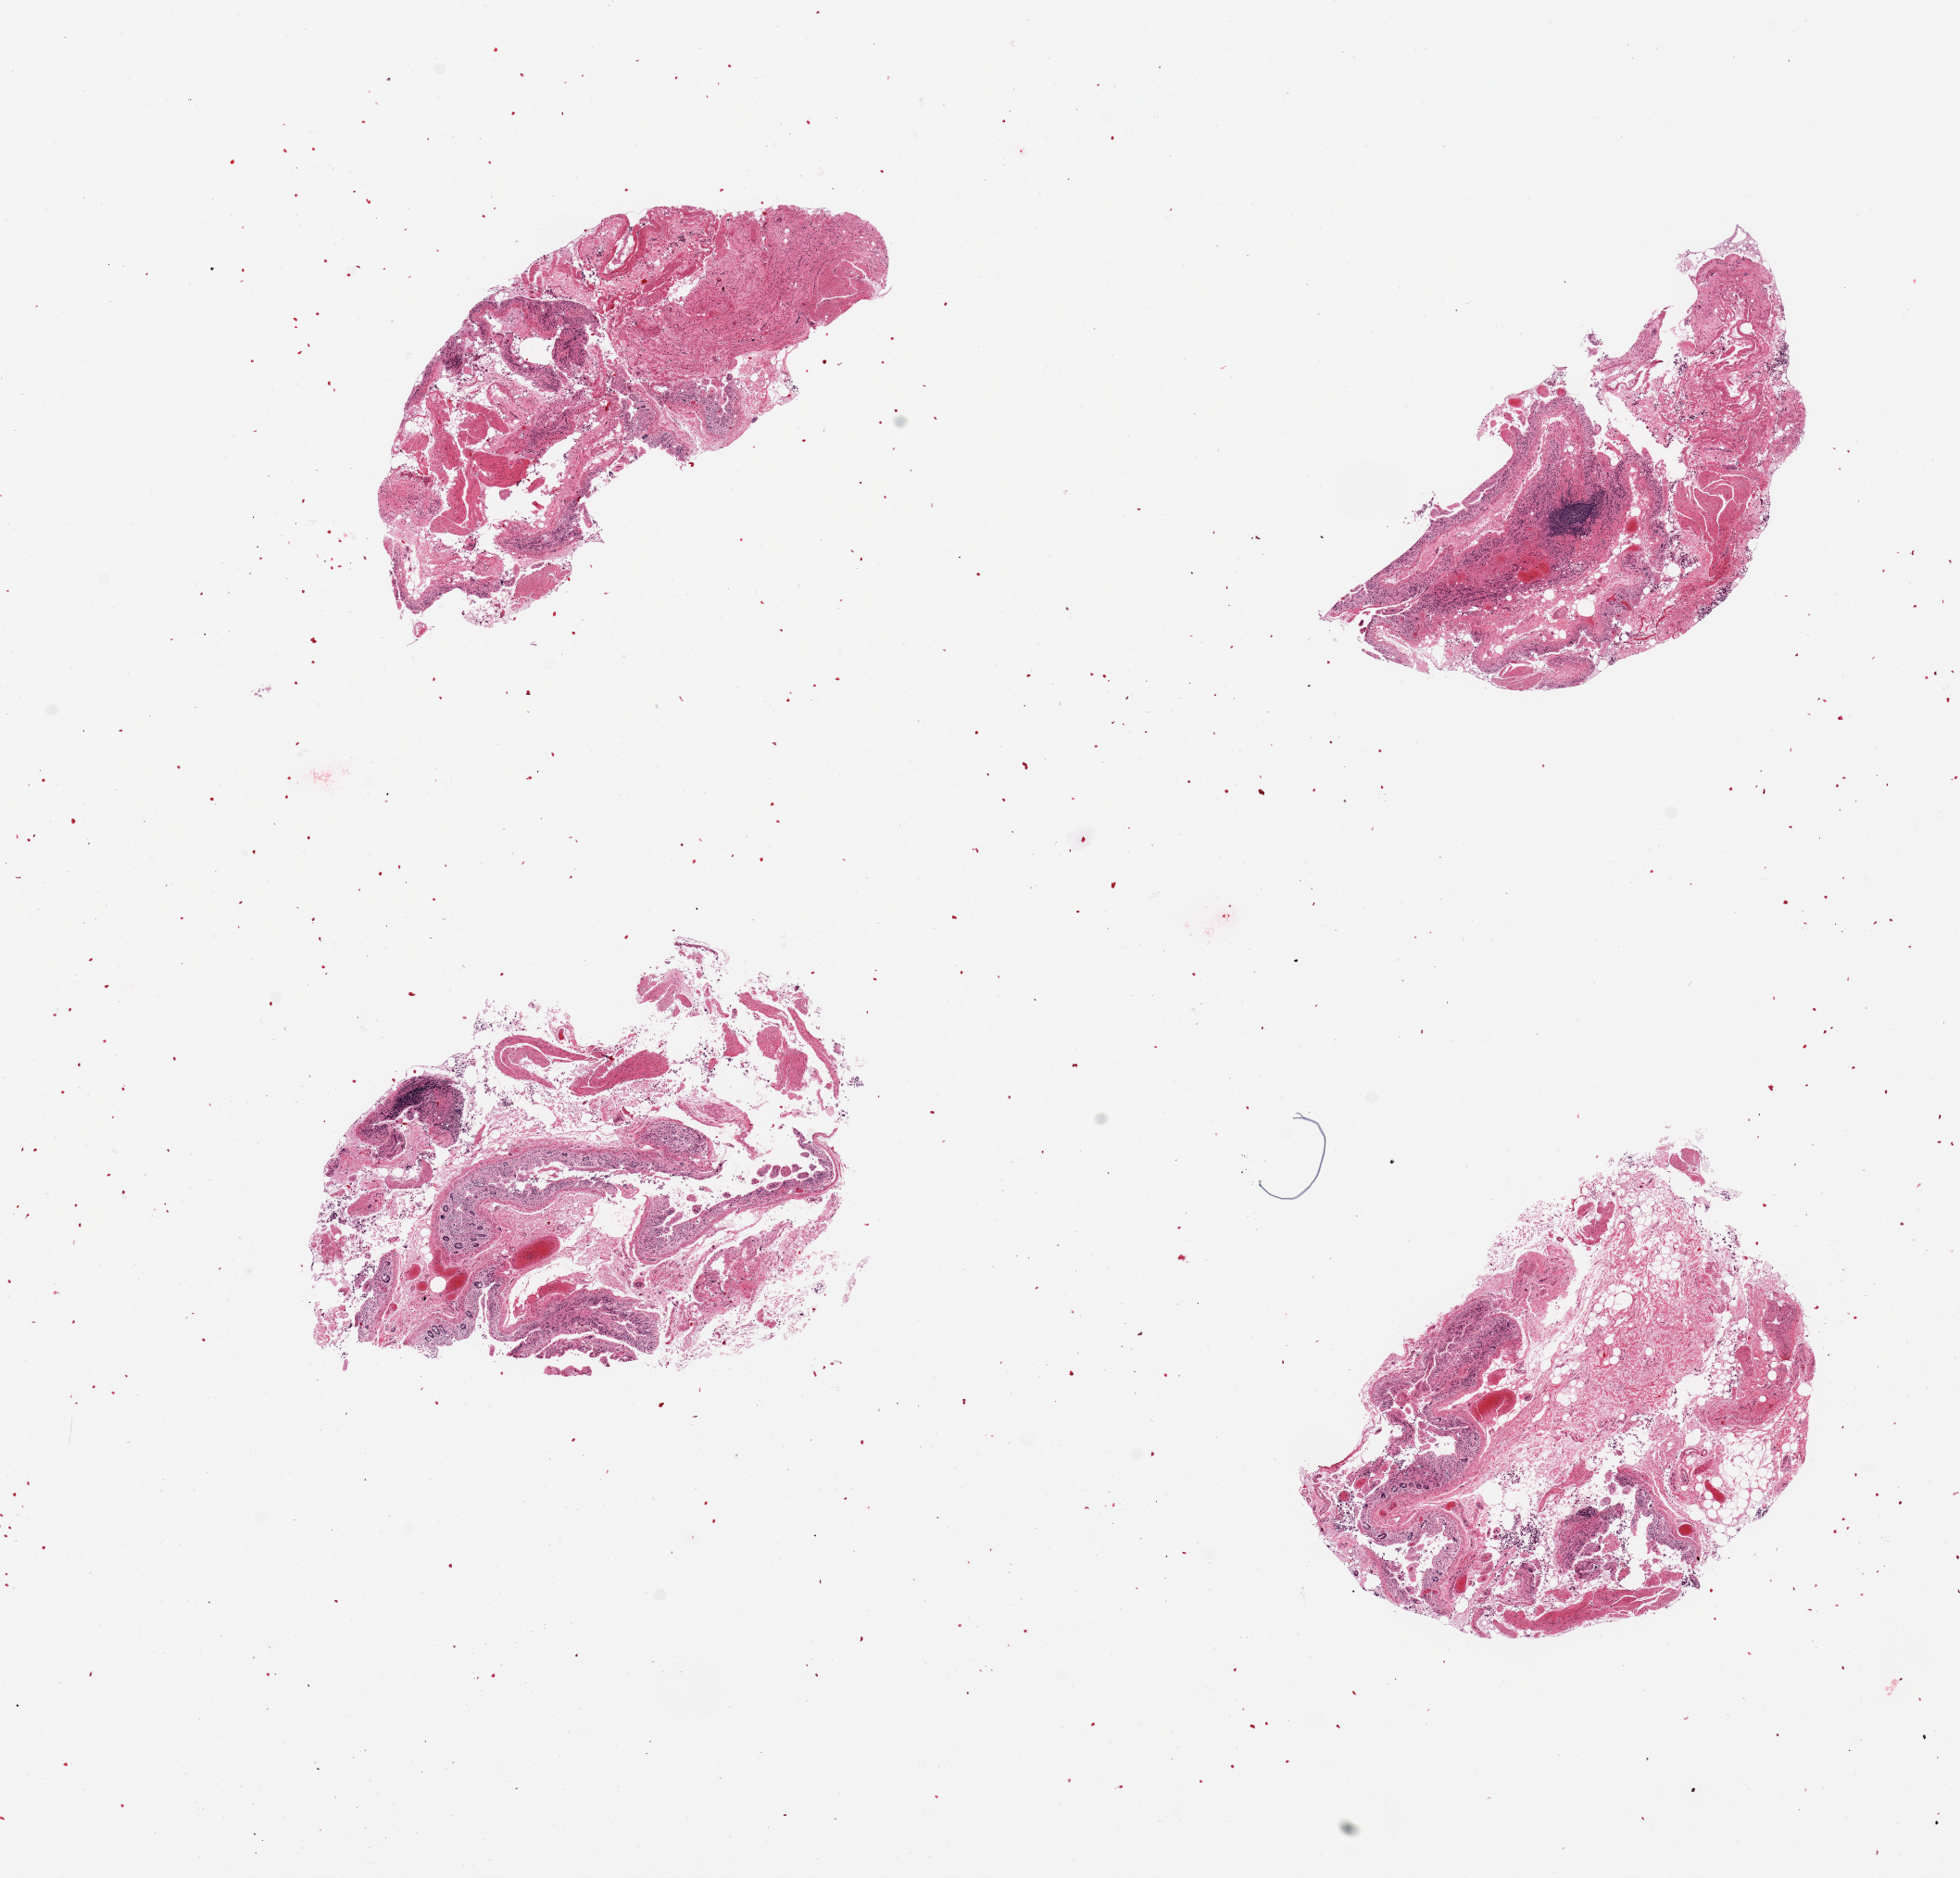
Digitized haematoxylin and eosin-stained section, a low-resolution overview of the entire scanned area, about 16.7 x 16.0 mm (from a 20x scan). Female donor.
- specimen: PAXgene-fixed, paraffin-embedded tissue; sampled site (target tissue): ileum; donor tissue sample